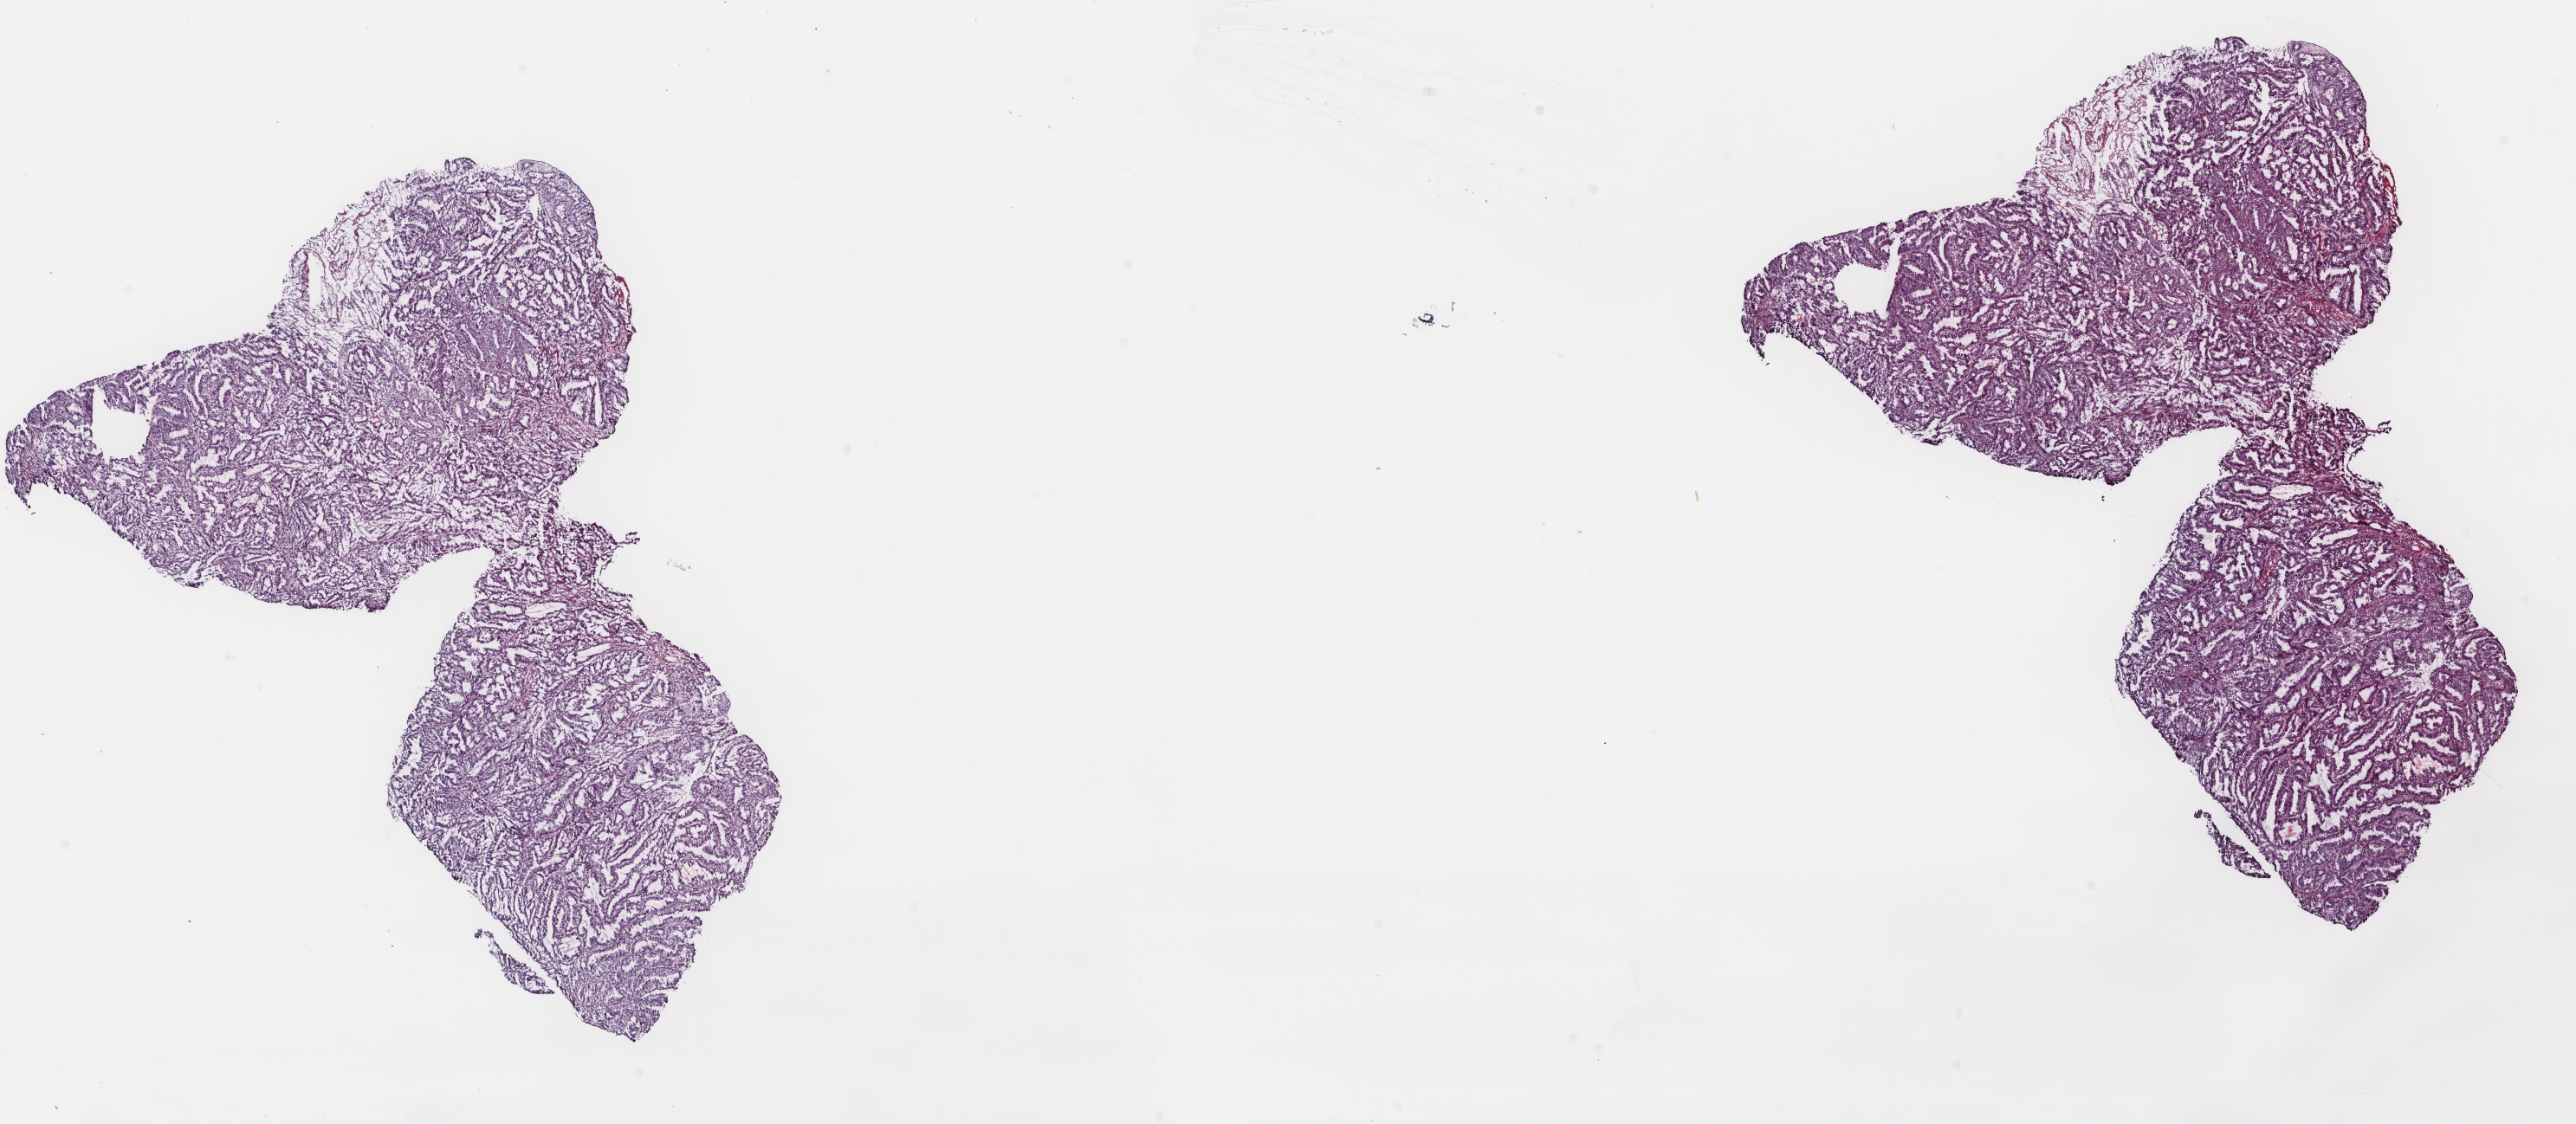
Digitized H&E tissue section (whole slide), whole scanned area (about 23.6 x 10.3 mm, from a 40x scan) shown as a low-resolution overview. Frozen section from the top of the tissue portion. Primary tumour sample from the uterus. Female patient; age at initial diagnosis 55 years. Histologic grade: G1 (well differentiated). Pathologist review of this section (percent, as recorded): tumour cells 70%, tumour nuclei 70%, normal cells 0%, stromal cells 30%, necrosis 0%. Inflammatory infiltration, as recorded: lymphocyte infiltration 20%, monocyte infiltration 0%, neutrophil infiltration 0%.
Pathologic diagnosis: Endometrioid adenocarcinoma, NOS. FIGO stage: IIIA.